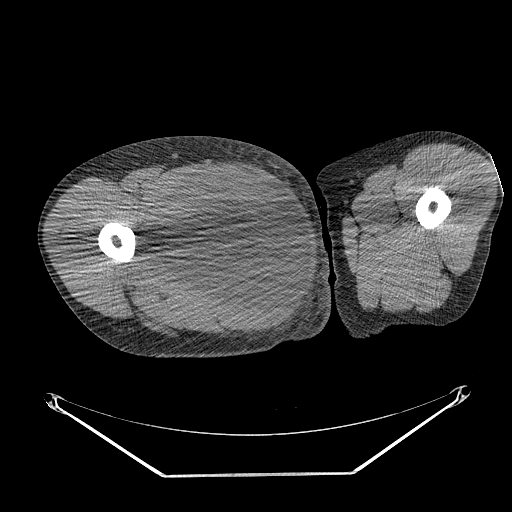
CT of an extremity soft-tissue mass (from a PET/CT study), one axial slice; slice 260 of 311 in the series (ordered by position); soft-tissue window (W 400 / L 40 HU); 3.75 mm slice thickness; 512 × 512 image matrix, field of view 500 × 500 mm. Male patient. Case-level facts recorded for this patient, not image findings: histological type: undifferentiated - pleiomorphic; grade: high; site of the primary tumour: right thigh.
Outlined on this slice (expert contour drawn on MRI and transferred to this co-registered scan by the dataset authors):
- gross tumour volume including surrounding oedema: bounding box [x1, y1, x2, y2] px = [142, 166, 268, 280]
- gross tumour volume (mass): [153, 169, 268, 275]